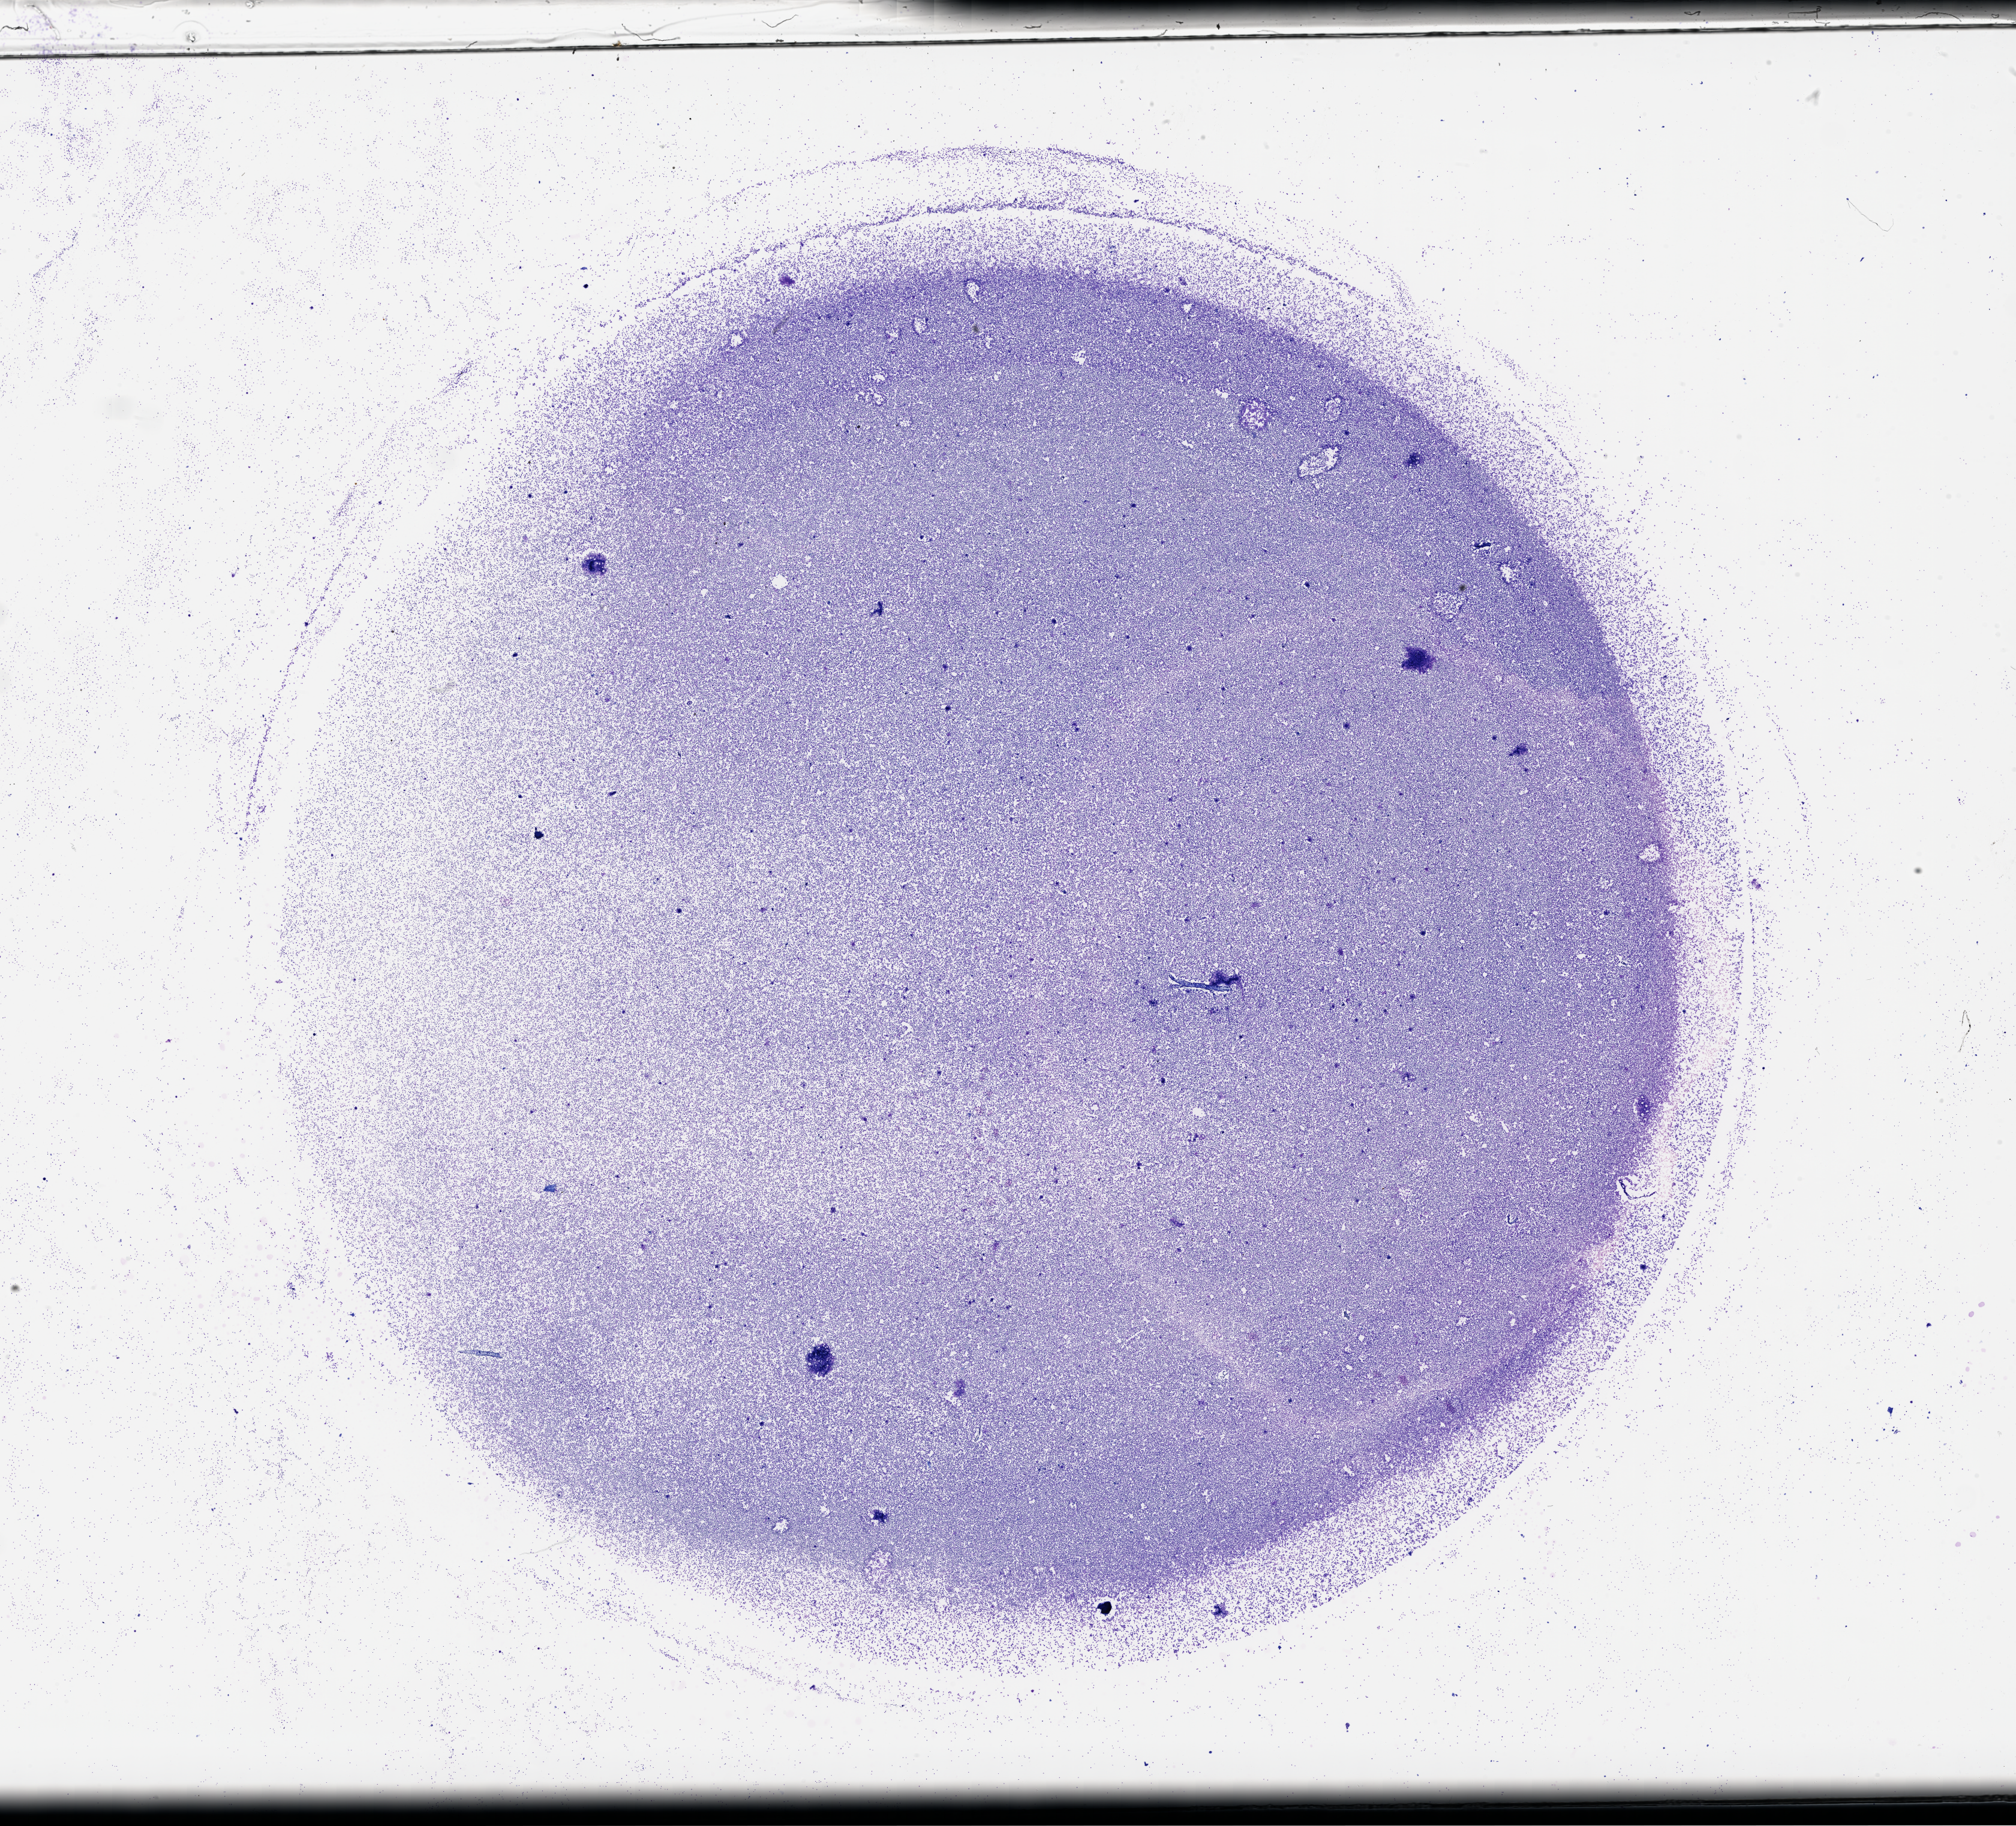
Hematoxylin and eosin (H&E) stained whole-slide image, low-resolution overview of the scanned area, about 27.1 x 24.6 mm; bone marrow (leukaemic) sample. Male, 45 y/o. Blasts: 90%.
• FAB classification: M4
• diagnosis: Acute Myeloid Leukemia
• WHO classification: Acute myelomonocytic leukemia